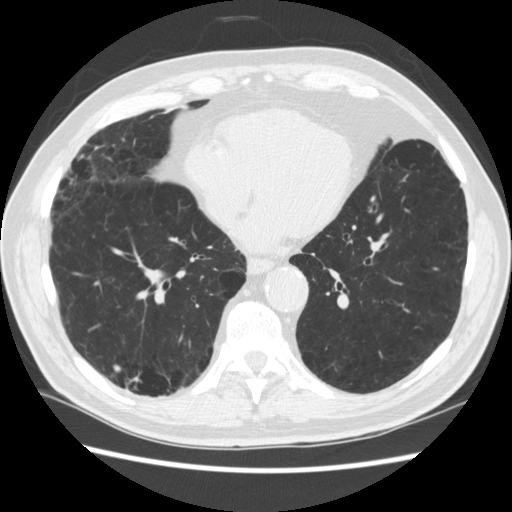
Low-dose screening chest CT, axial slice; third screening round (two years after baseline); lung window (W 1500 / L -600 HU); 1.25 mm slice thickness; standard (soft-tissue) reconstruction kernel (STANDARD). Male participant, aged 70 years at enrolment.
Lesion marked by an expert reader, bounding box <131,358,175,411> (left, top, right, bottom; pixels). The screening reader recorded 4 non-calcified nodules or masses ≥4 mm on this exam (right lower lobe, right lower lobe, left lower lobe, left lower lobe); which of them this box marks is not recorded. Participant outcome: lung cancer diagnosed 253 days after this screen — squamous cell carcinoma, NOS, right upper lobe, poorly differentiated (G3), stage IV (AJCC 6th edition).